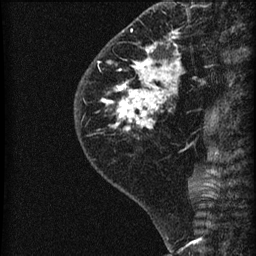
Breast MRI (dynamic contrast-enhanced), one sagittal slice. Position 21 of 60 along the scan axis. Dynamic contrast-enhanced series, image 2 of 3 at this slice position (ordered by acquisition). 1.5 T. TE 4.2 ms, TR 22.7 ms. 256 × 256 image matrix, field of view 180 × 180 mm. Female patient, age 45 years. From the clinical record (not read from this slice): setting: breast cancer imaged before/during neoadjuvant chemotherapy; receptor status: HR-positive, HER2-negative.
Structures marked on this image (semi-automatic segmentation, software-assisted and operator-edited):
- analysis volume of interest (the breast-tissue region the enhancement analysis was run in; not a lesion): bounding box (x1, y1, x2, y2) in pixels: (74, 11, 205, 140)
- tumour enhancement mask (voxels above the 90 % enhancement threshold inside the analysis volume of interest): (114, 31, 179, 131)